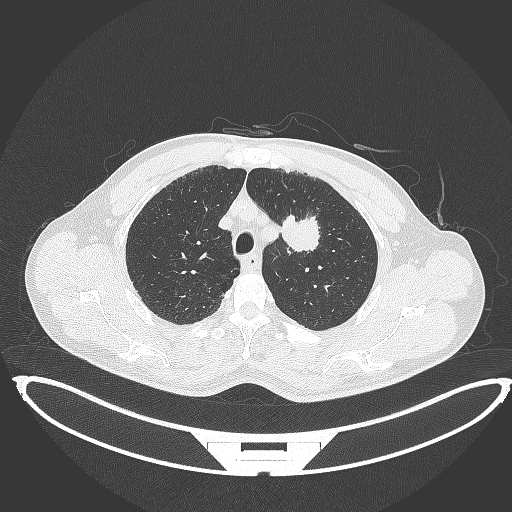
Chest CT, one axial slice. Position 346 of 395 along the scan axis. 120 kVp. Lung window (W 1500 / L -600 HU). 1 mm slice thickness. 512 × 512 image matrix, field of view 457 × 457 mm. Patient: male, 60 years. Case-level facts recorded for this patient, not image findings: clinical TNM (as recorded): T2a N0 M0.
Outlined on this slice (bounding box drawn by a radiologist):
- lung tumour (recorded histology: squamous cell carcinoma): bounding box <281,213,321,257> (left, top, right, bottom; pixels)